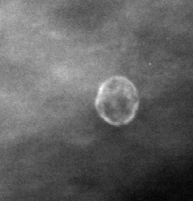
Crop from a digitized film mammogram around one marked abnormality; left breast; MLO view.
Calcifications, morphology lucent center; BI-RADS assessment category 2; benign without callback (not worked up further).